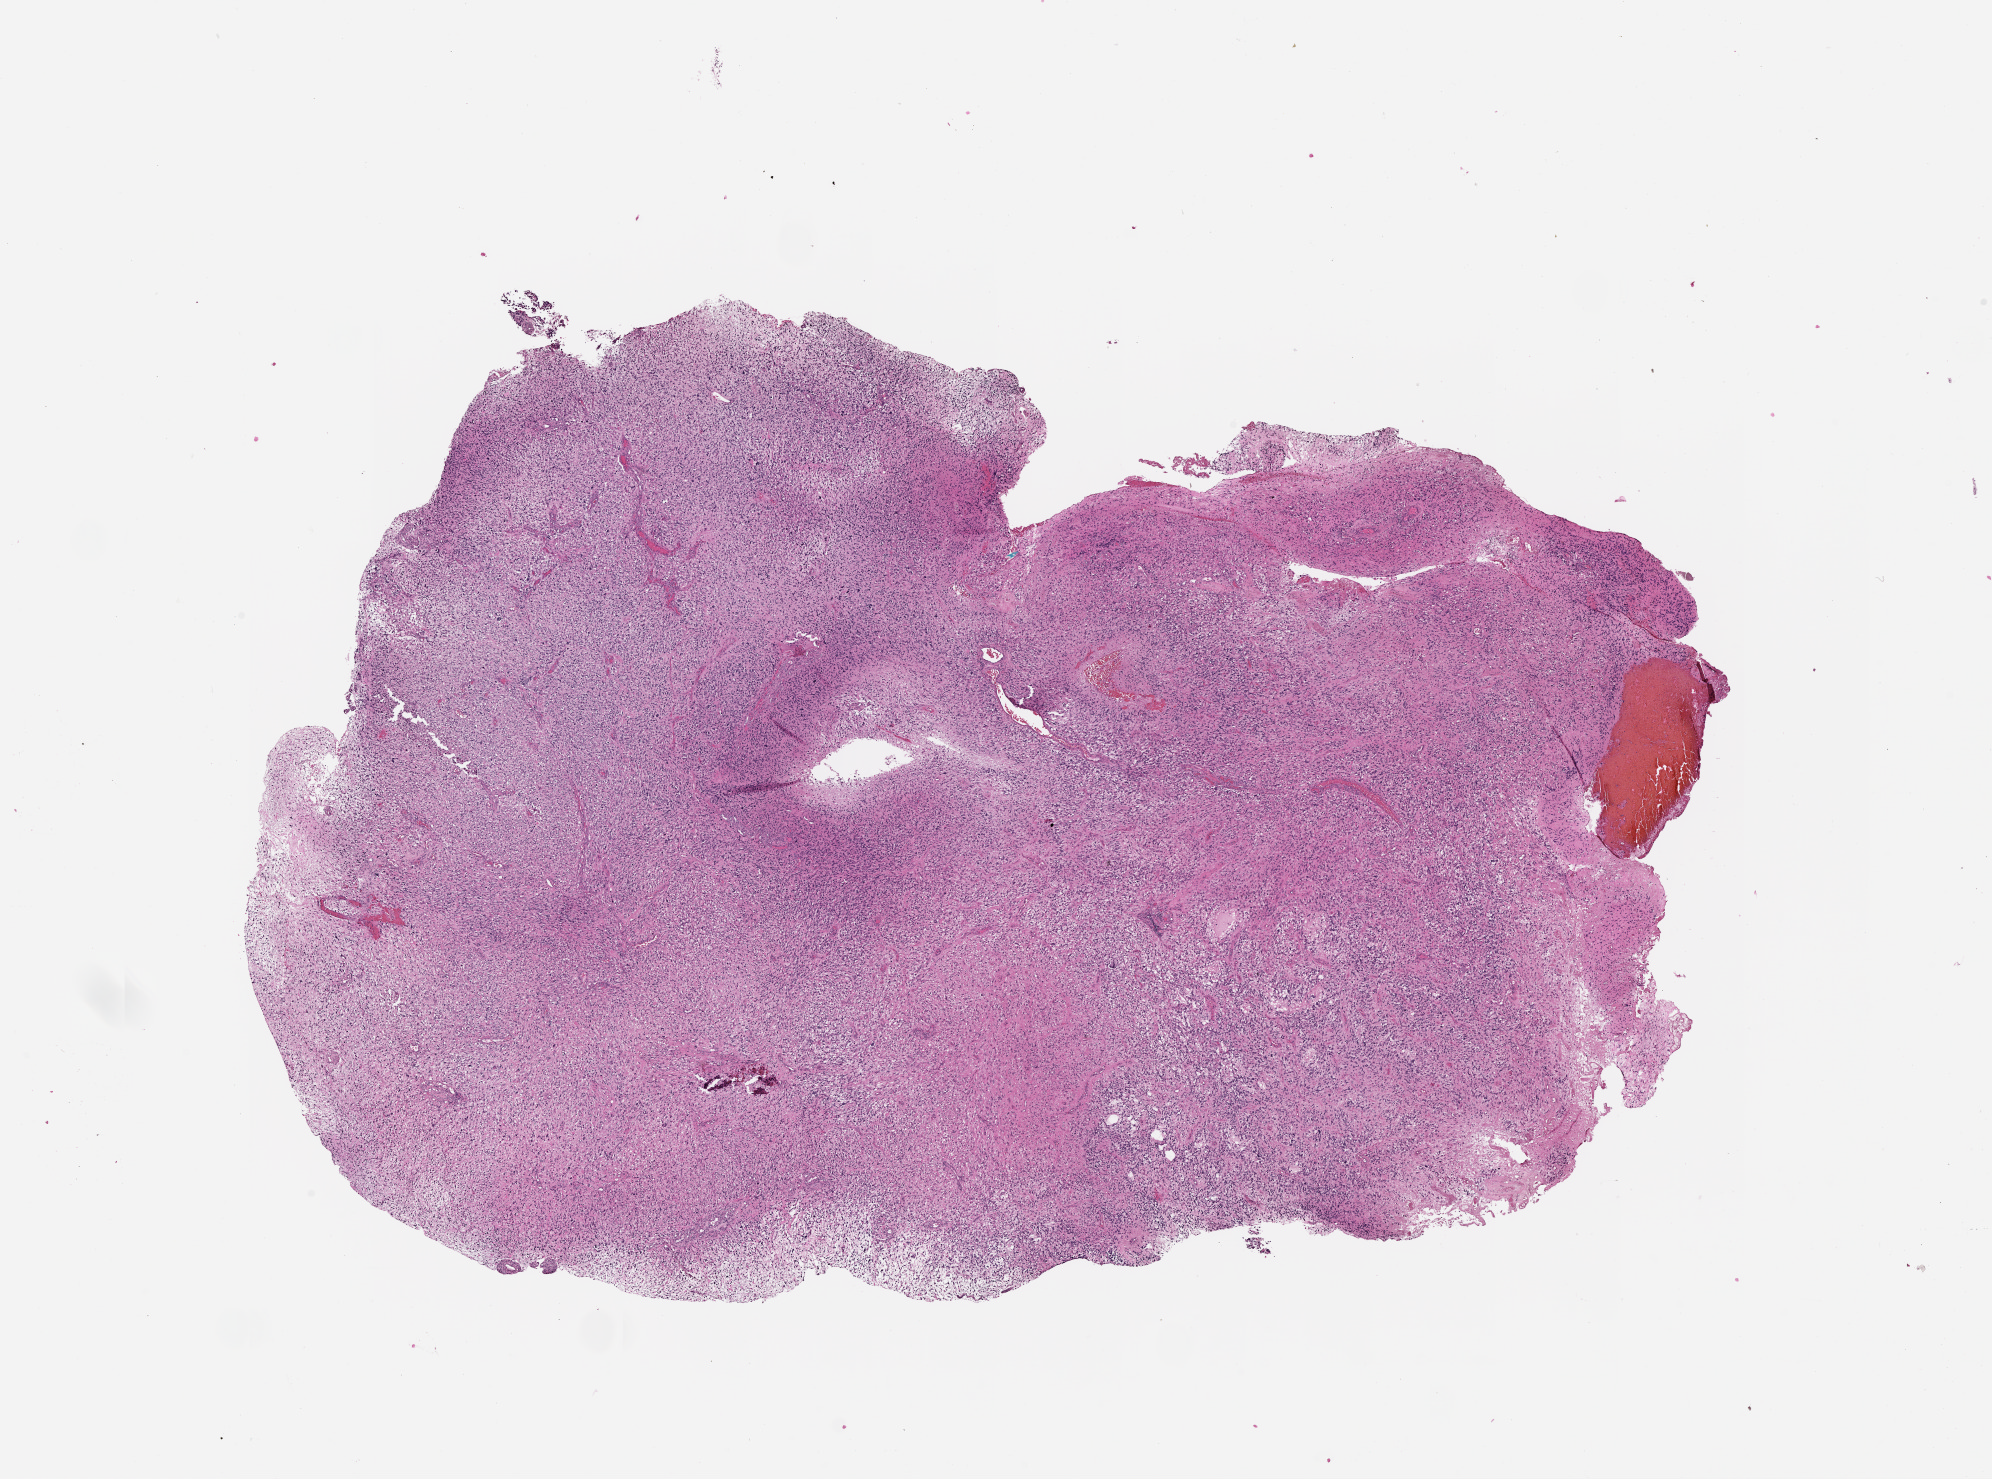
Hematoxylin and eosin (H&E) stained whole-slide image — a low-resolution overview of the entire scanned area, about 16.0 x 11.9 mm (acquisition: 20x scan). Tumour tissue sample, brain. 31-year-old male patient.
* histologic diagnosis: Glioblastoma
* primary tumour site (as recorded): frontal lobe